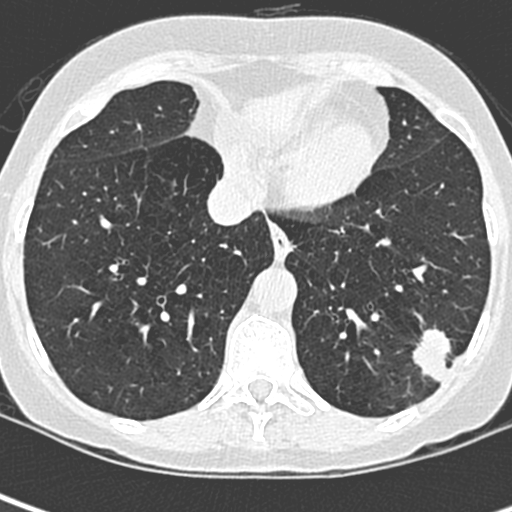
Low-dose screening chest CT, one axial slice; position 87 of 252 along the scan axis; 120 kVp; lung window (W 1500 / L -600 HU); 1.3 mm slice thickness; 512 × 512 image matrix, field of view 271 × 271 mm.
Outlined on this slice (expert manual segmentation):
- lesion 1 (tumor, lower lobe of left lung): bounding box [x1, y1, x2, y2] px = [412, 328, 451, 383]